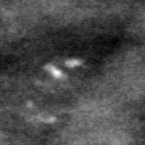
Region of interest cut from a scanned film mammogram (one marked finding), right breast, CC view, BI-RADS breast density category 3 (scale 1–4).
- Finding: calcifications, morphology pleomorphic, distribution clustered; BI-RADS assessment category 4; pathology result (as recorded, not read from the image): benign.